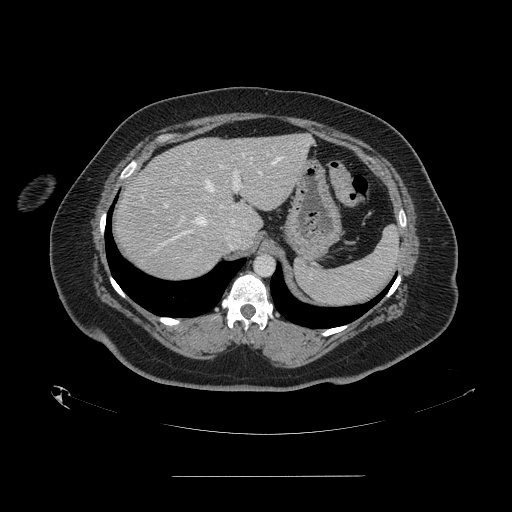
Contrast-enhanced abdominal CT, one axial slice; slice 114 of 164 in the series (ordered by position); intravenous contrast given; soft-tissue window (W 400 / L 40 HU); 2.5 mm slice thickness; 512 × 512 image matrix. Female patient, age 52 years. From the clinical record (not read from this slice): diagnosis: colorectal cancer liver metastases, imaged before liver resection; multiple liver metastases: yes; largest metastasis: 3.5 cm; chemotherapy before resection: no.
Structures marked on this image (outlined manually by an expert reader):
- hepatic veins: box from (x=155, y=156) to (x=284, y=246) px
- liver: (x=114, y=135)–(x=312, y=281)
- planned liver remnant (the part of the liver to remain after resection): (x=170, y=135)–(x=312, y=226)
- portal vein (with intrahepatic branches): (x=164, y=171)–(x=241, y=207)